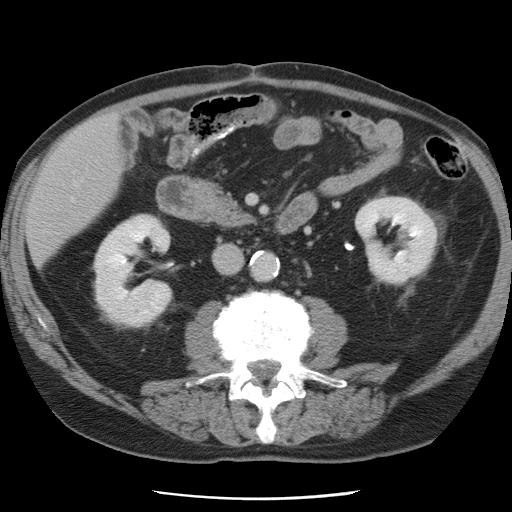
Contrast-enhanced abdominal CT, one axial slice. Position 22 of 78 along the scan axis. Intravenous contrast given. Soft-tissue window (W 400 / L 40 HU). 5 mm slice thickness. 512 × 512 image matrix, field of view 337 × 337 mm. Male patient, age 75 years. From the clinical record (not read from this slice): diagnosis: colorectal cancer liver metastases, imaged before liver resection; multiple liver metastases: yes; largest metastasis: 2.4 cm; chemotherapy before resection: yes.
Annotated regions visible in this slice (manually delineated by an expert):
- liver: bounding box <27,116,117,263> (left, top, right, bottom; pixels)
- planned liver remnant (the part of the liver to remain after resection): <27,120,119,262>